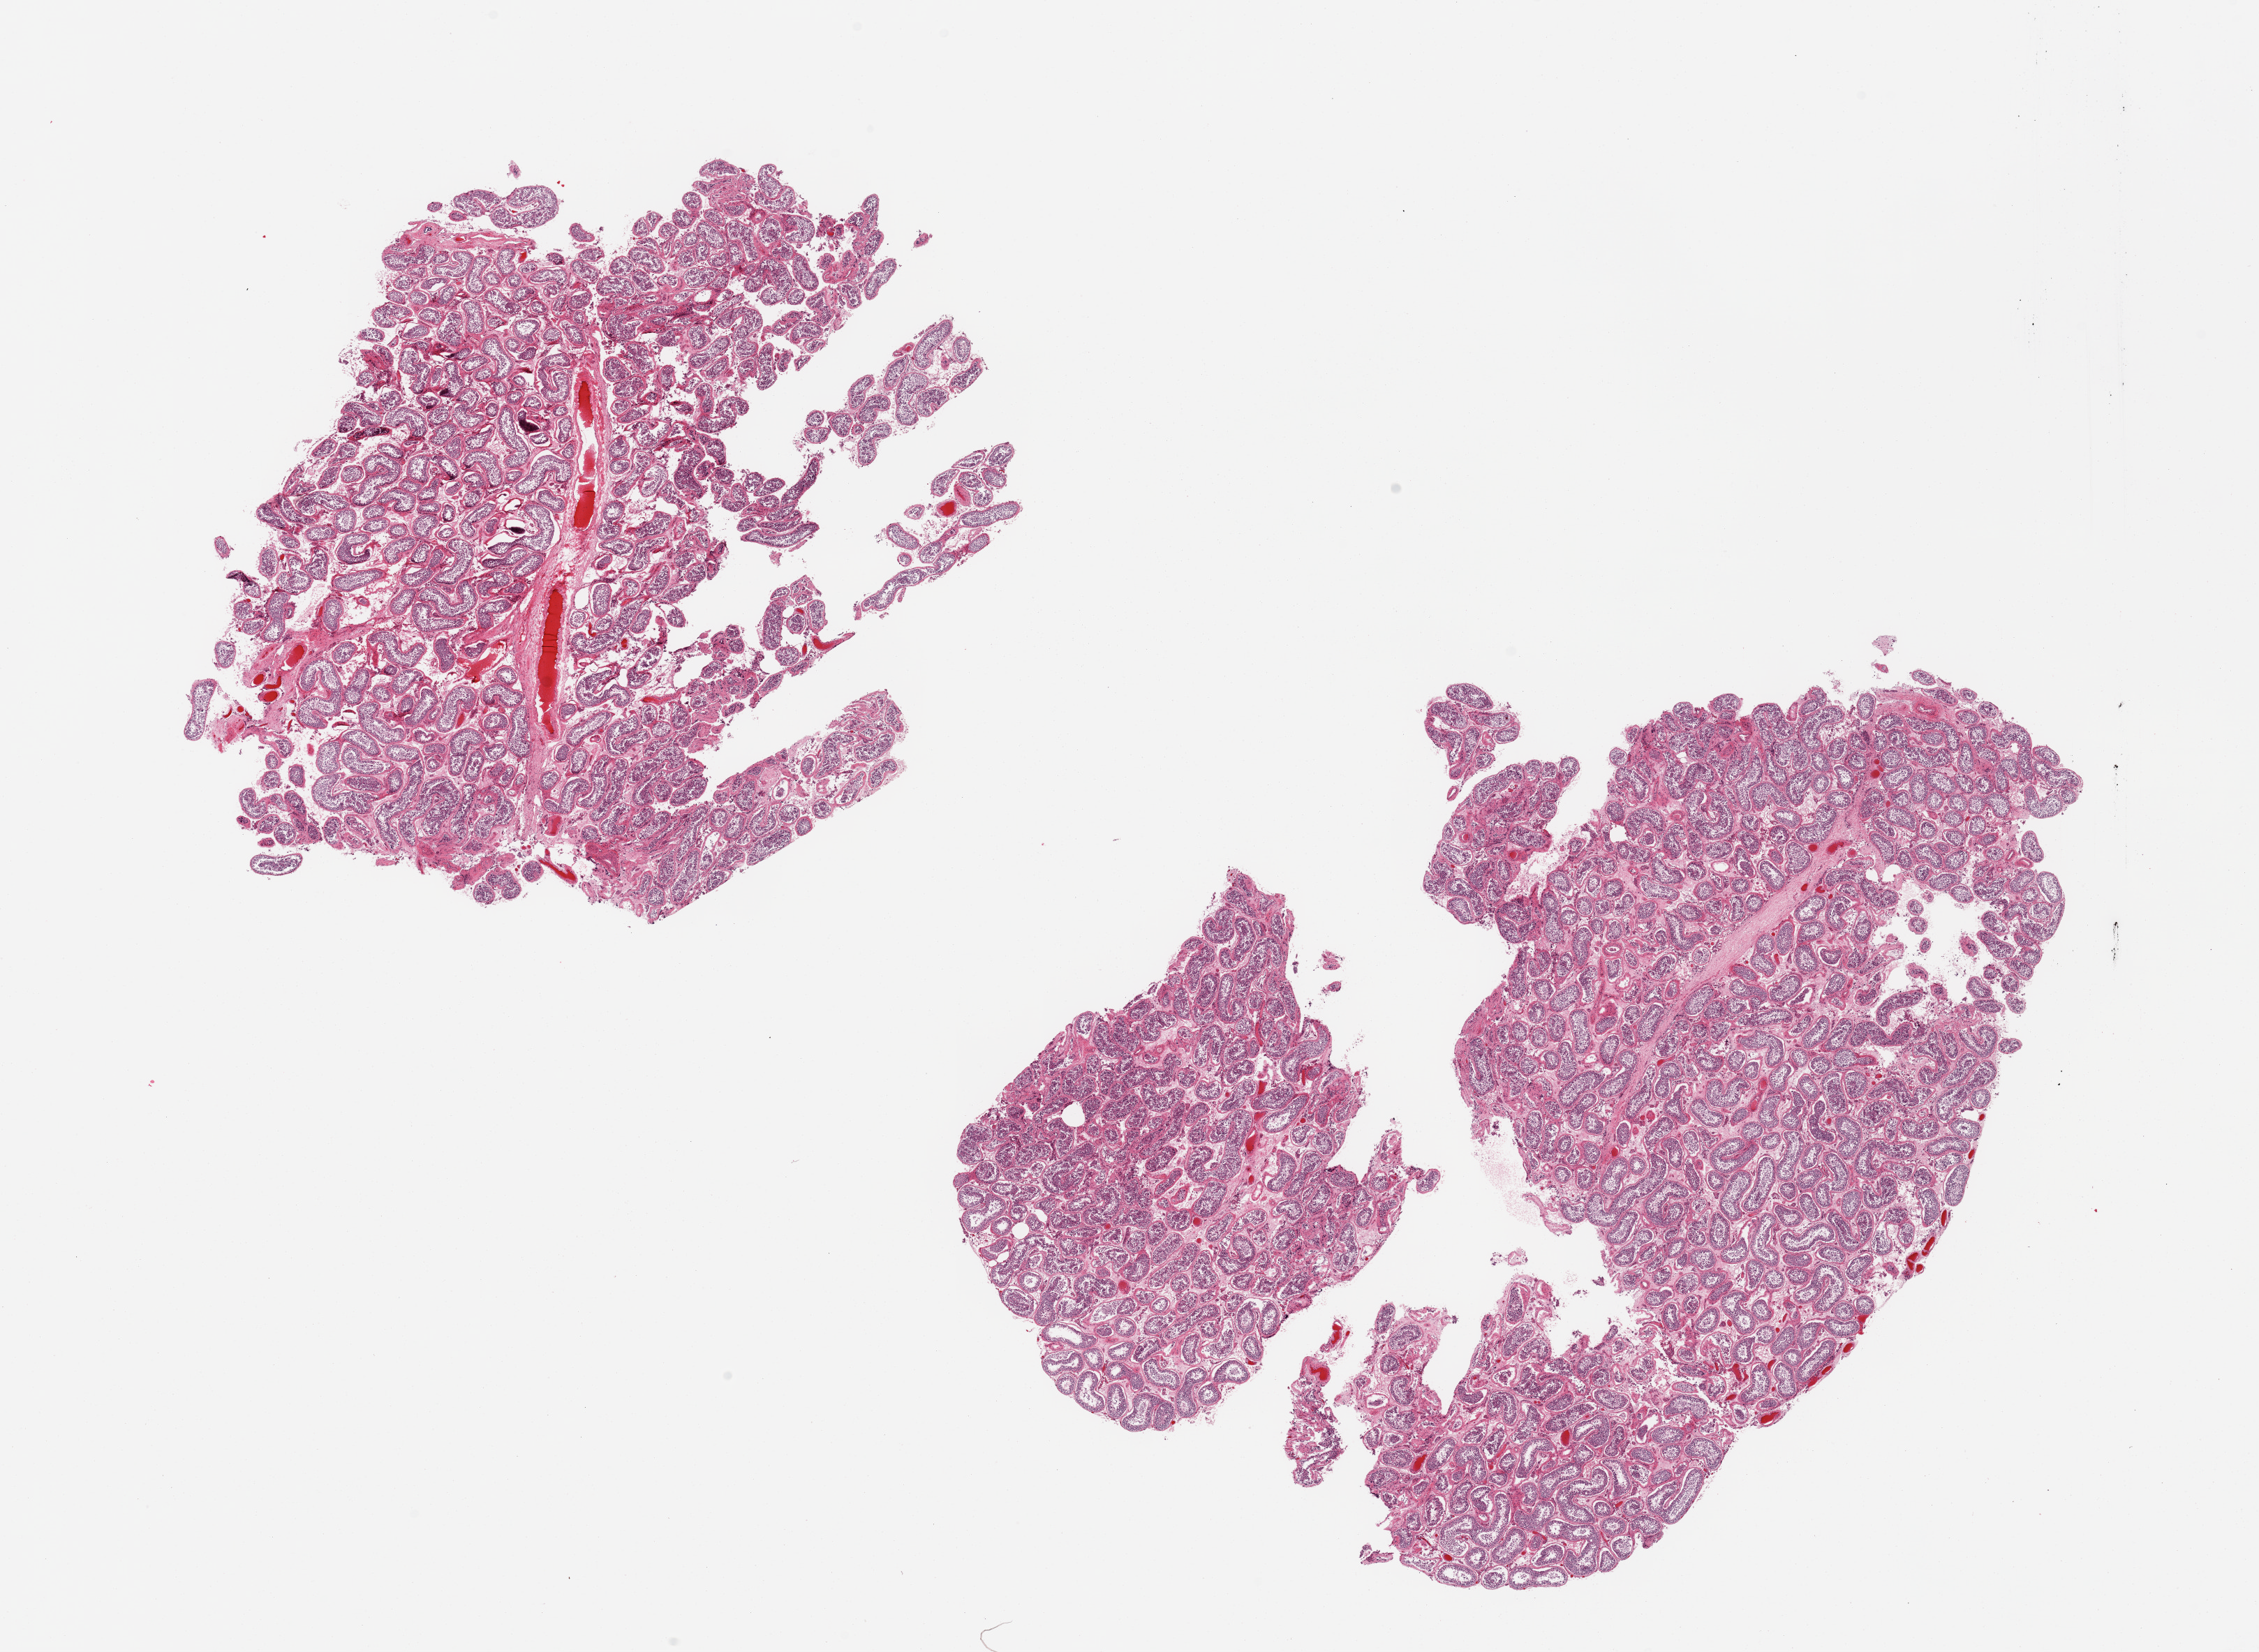
Whole-slide image, hematoxylin and eosin (H&E) stain, low-resolution overview of the scanned area, about 25.6 x 18.7 mm. PAXgene-fixed, paraffin-embedded tissue. Target tissue: testis. Tissue donor sample.
* reviewer comment on this tissue sample: 2 pieces; spermatogenesis